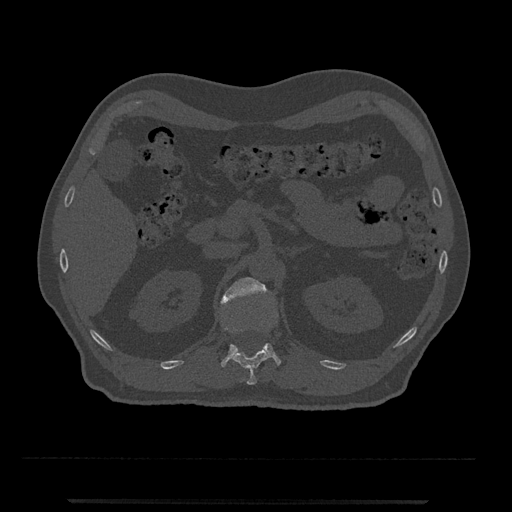
CT including the spine, one axial slice. Slice 371 of 797 in the series (ordered by position). Reconstruction kernel Br40s/3. 120 kVp. Bone window (W 1800 / L 400 HU). 0.5 mm slice thickness. 512 × 512 image matrix, field of view 419 × 419 mm. Male patient, age 63 years. From the clinical record (not read from this slice): primary cancer: prostate.
Annotated regions visible in this slice (semi-automatic segmentation, software-assisted and operator-edited):
- L1 vertebra: bounding box <220,277,281,367> (left, top, right, bottom; pixels)
- T12 vertebra: <223,308,270,385>